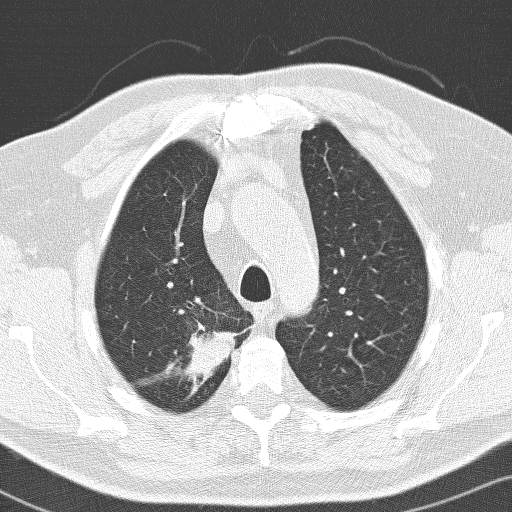
Low-dose screening chest CT, axial slice. Baseline annual screen. Lung window (W 1500 / L -600 HU). 3.2 mm slice thickness. Lung (sharp) reconstruction kernel (D). 512 × 512 image matrix, field of view 326 × 326 mm. Male participant, aged 66 years at enrolment. Former smoker at enrolment.
• Expert reader's lesion annotation, bounding box (x1, y1, x2, y2) in pixels: (153, 312, 231, 393).
• Reader record for this screening exam (exam-level; its link to the box is not recorded): non-calcified nodule or mass ≥4 mm, right upper lobe, 36 × 30 mm, spiculated (stellate) margins, soft tissue attenuation.
• Official screen result: positive, change unspecified: nodule(s) >= 4 mm or enlarging nodule(s), mass(es), or other non-specific abnormalities suspicious for lung cancer.
• Later outcome: lung cancer diagnosed 103 days after this screen — adenocarcinoma, NOS, right upper lobe, poorly differentiated (G3), stage IIB (AJCC 6th edition), 33 mm at pathology.